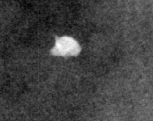
Region of interest cut from a scanned film mammogram (one marked finding); right breast; CC view.
- Finding: calcifications, morphology round and regular / lucent center / punctate, distribution diffusely scattered; BI-RADS assessment category 2; benign; no additional work-up was recommended (benign without callback).